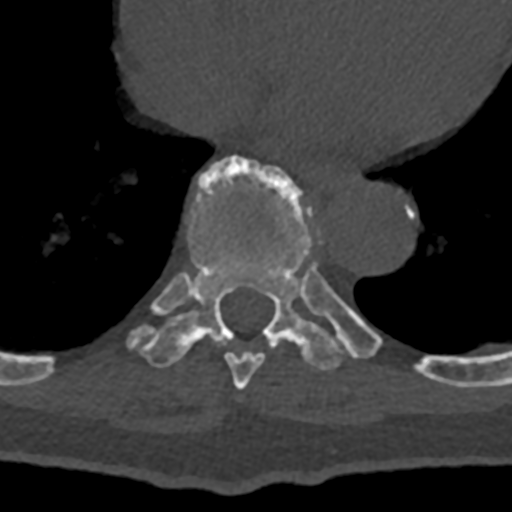
CT including the spine, one axial slice; position 676 of 797 along the scan axis; bone window (W 1800 / L 400 HU); 0.5 mm slice thickness; 512 × 512 image matrix. Male patient, age 74 years. Case-level facts recorded for this patient, not image findings: primary cancer: renal; vertebrae with lytic lesions (as recorded): T10, L1, L2, L3, L4, L5.
Annotated regions visible in this slice (semi-automatically segmented with operator editing):
- T8 vertebra: box from (x=225, y=291) to (x=332, y=390) px
- T9 vertebra: (x=128, y=157)–(x=432, y=379)